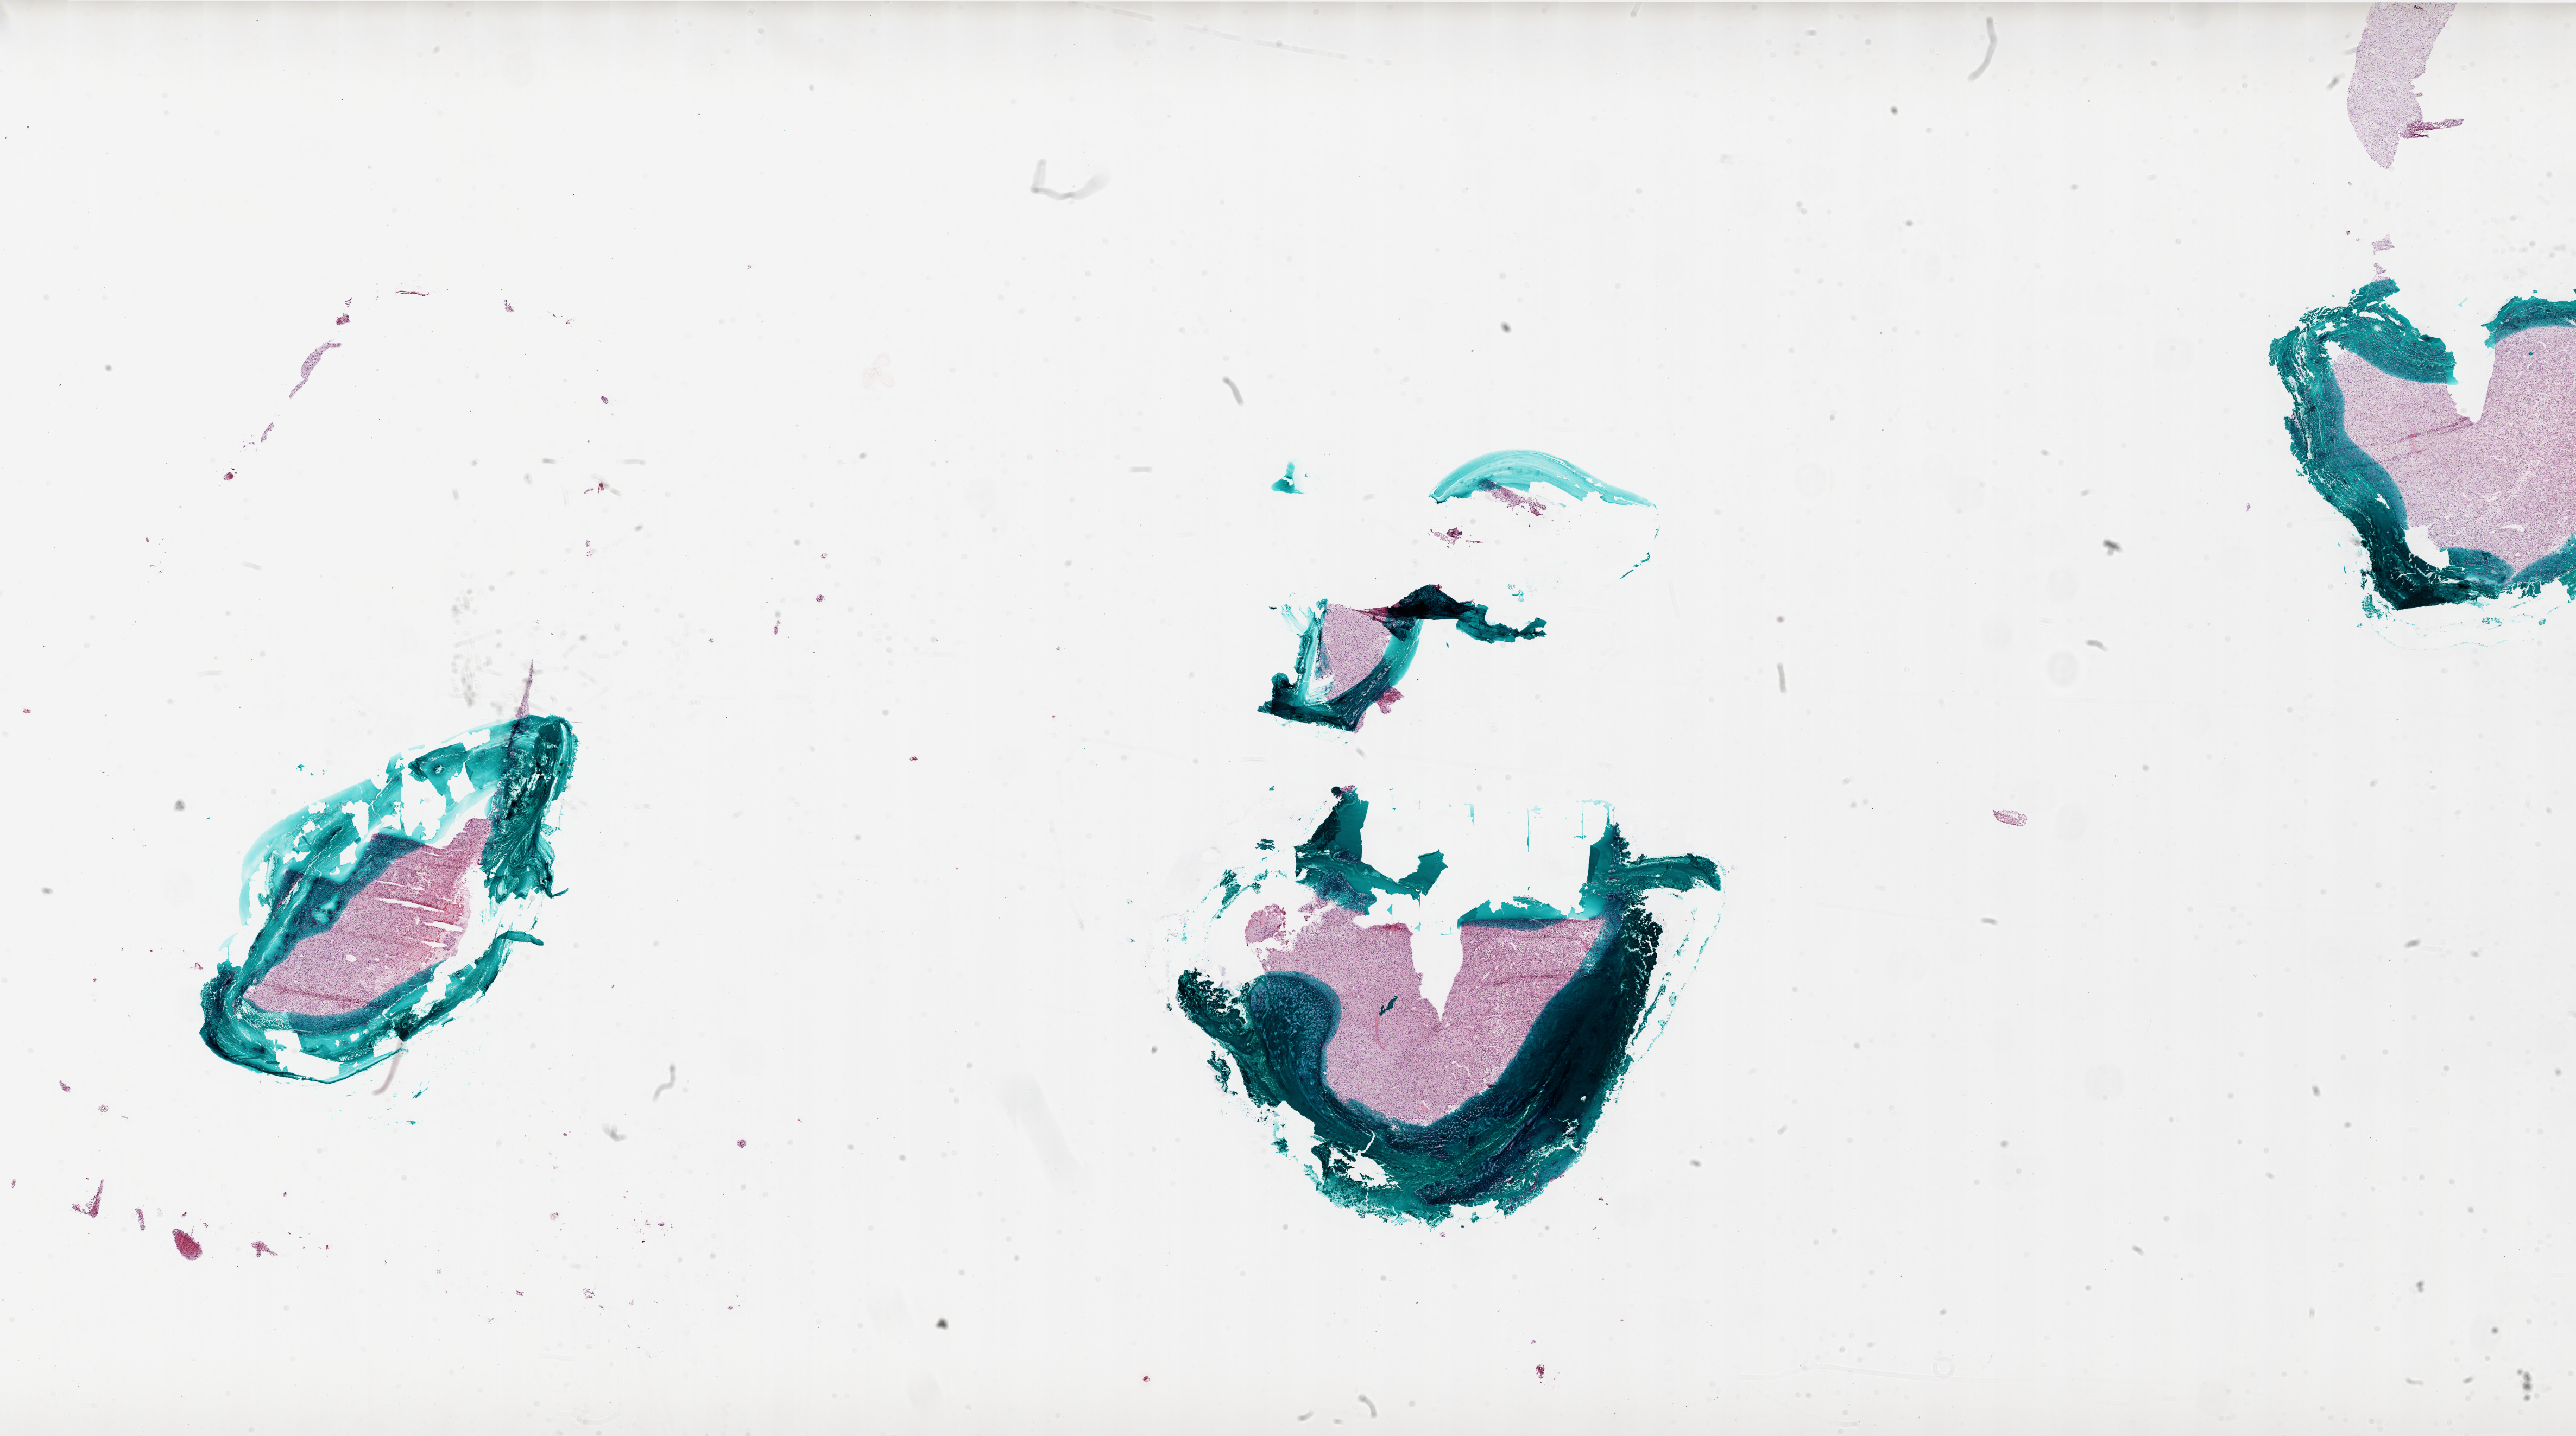
Whole-slide histology image, H&E — a low-resolution overview of the entire scanned area, about 38.0 x 21.2 mm (acquisition: 20x scan); frozen section; brain, primary tumour sample. Male, age 63 years at initial diagnosis. Pathologist review of this section (percent, as recorded): tumour cells 100%, tumour nuclei 100%.
Pathologic diagnosis: Glioblastoma.